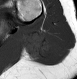
MRI of an extremity soft-tissue mass, one axial slice; slice 15 of 28 in the series (ordered by position); MR volume resampled by the dataset authors to the PET/CT grid (not the native acquisition matrix); 3.27 mm slice thickness; 77 × 79 image matrix. Female patient. Case-level facts recorded for this patient, not image findings: histological type: malignant fibrous histiocytoma; grade: low; site of the primary tumour: left arm.
Outlined on this slice (expert contour drawn on MRI and transferred to this co-registered scan by the dataset authors):
- gross tumour volume (mass): bounding box (x1, y1, x2, y2) in pixels: (22, 31, 57, 62)